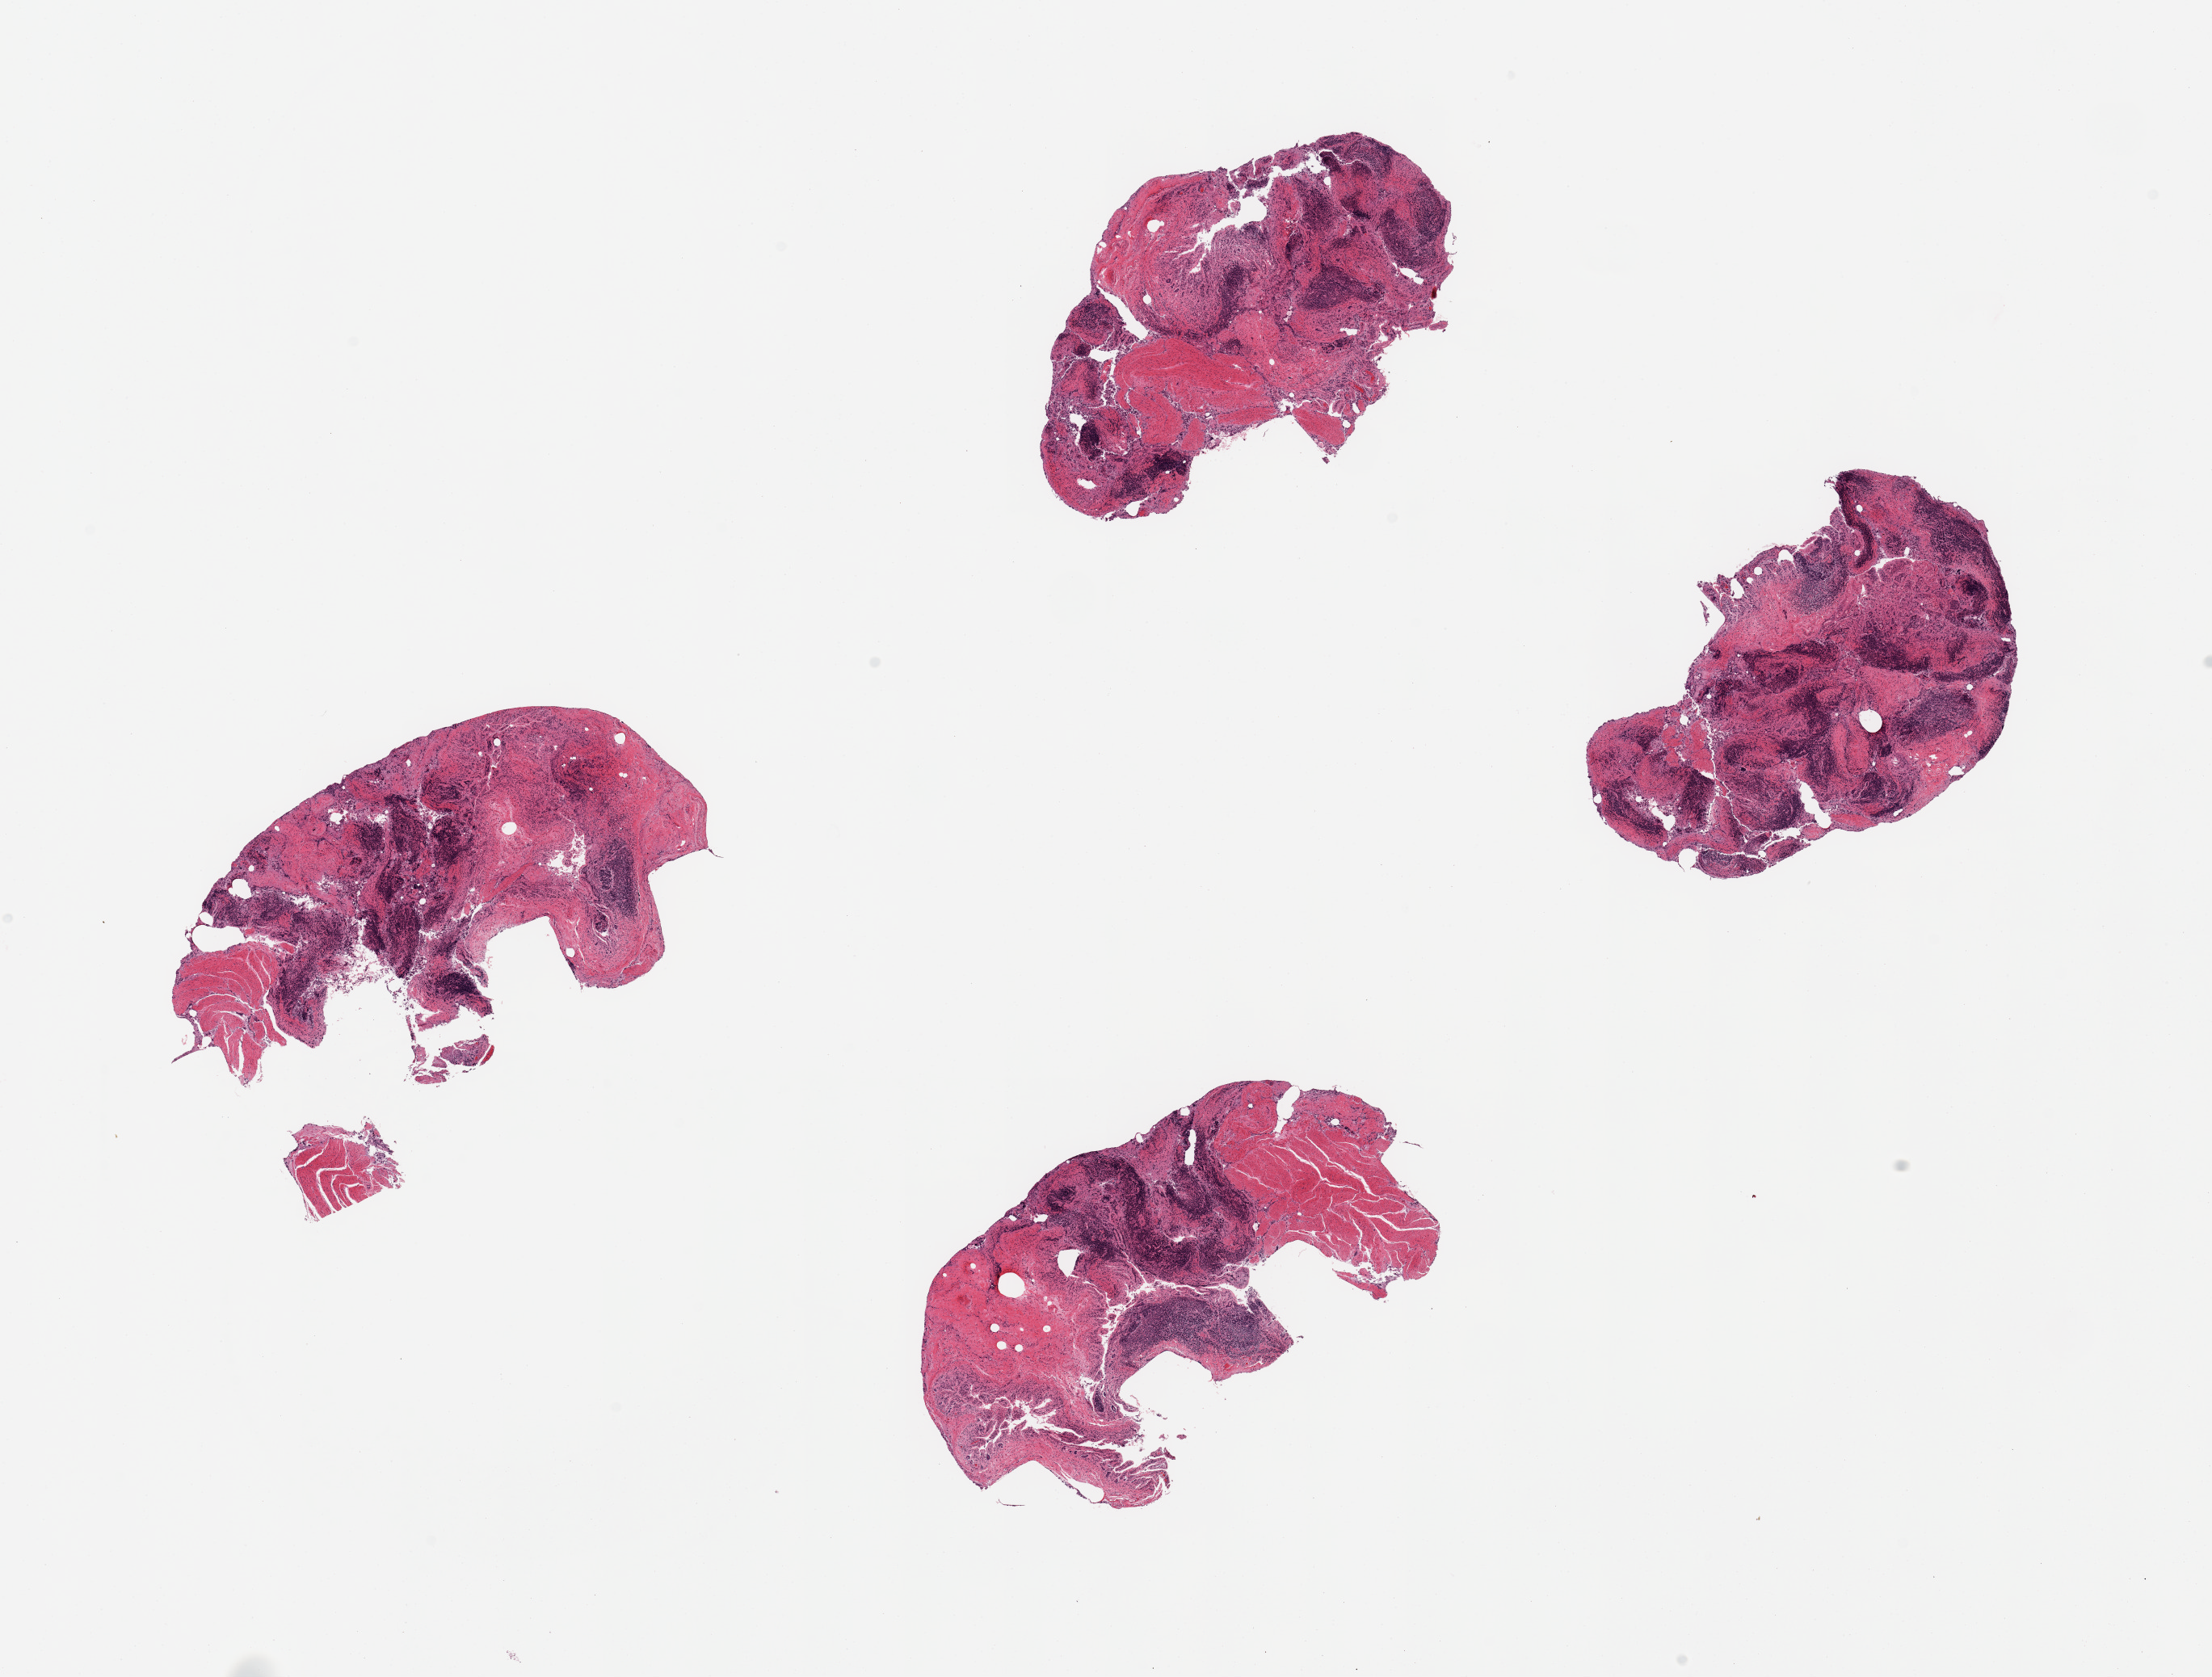
Whole-slide image, haematoxylin and eosin stain, low-resolution overview of the scanned area, about 21.7 x 16.4 mm. PAXgene-fixed, paraffin-embedded tissue. Section of ileum (target tissue). Tissue donor sample. Male donor.
• reviewer comment on this tissue sample: 4 pieces; glandular component of mucosa markedly autolyzed; residual lymphoid aggregates reasonably preserved, ~40% of tissue